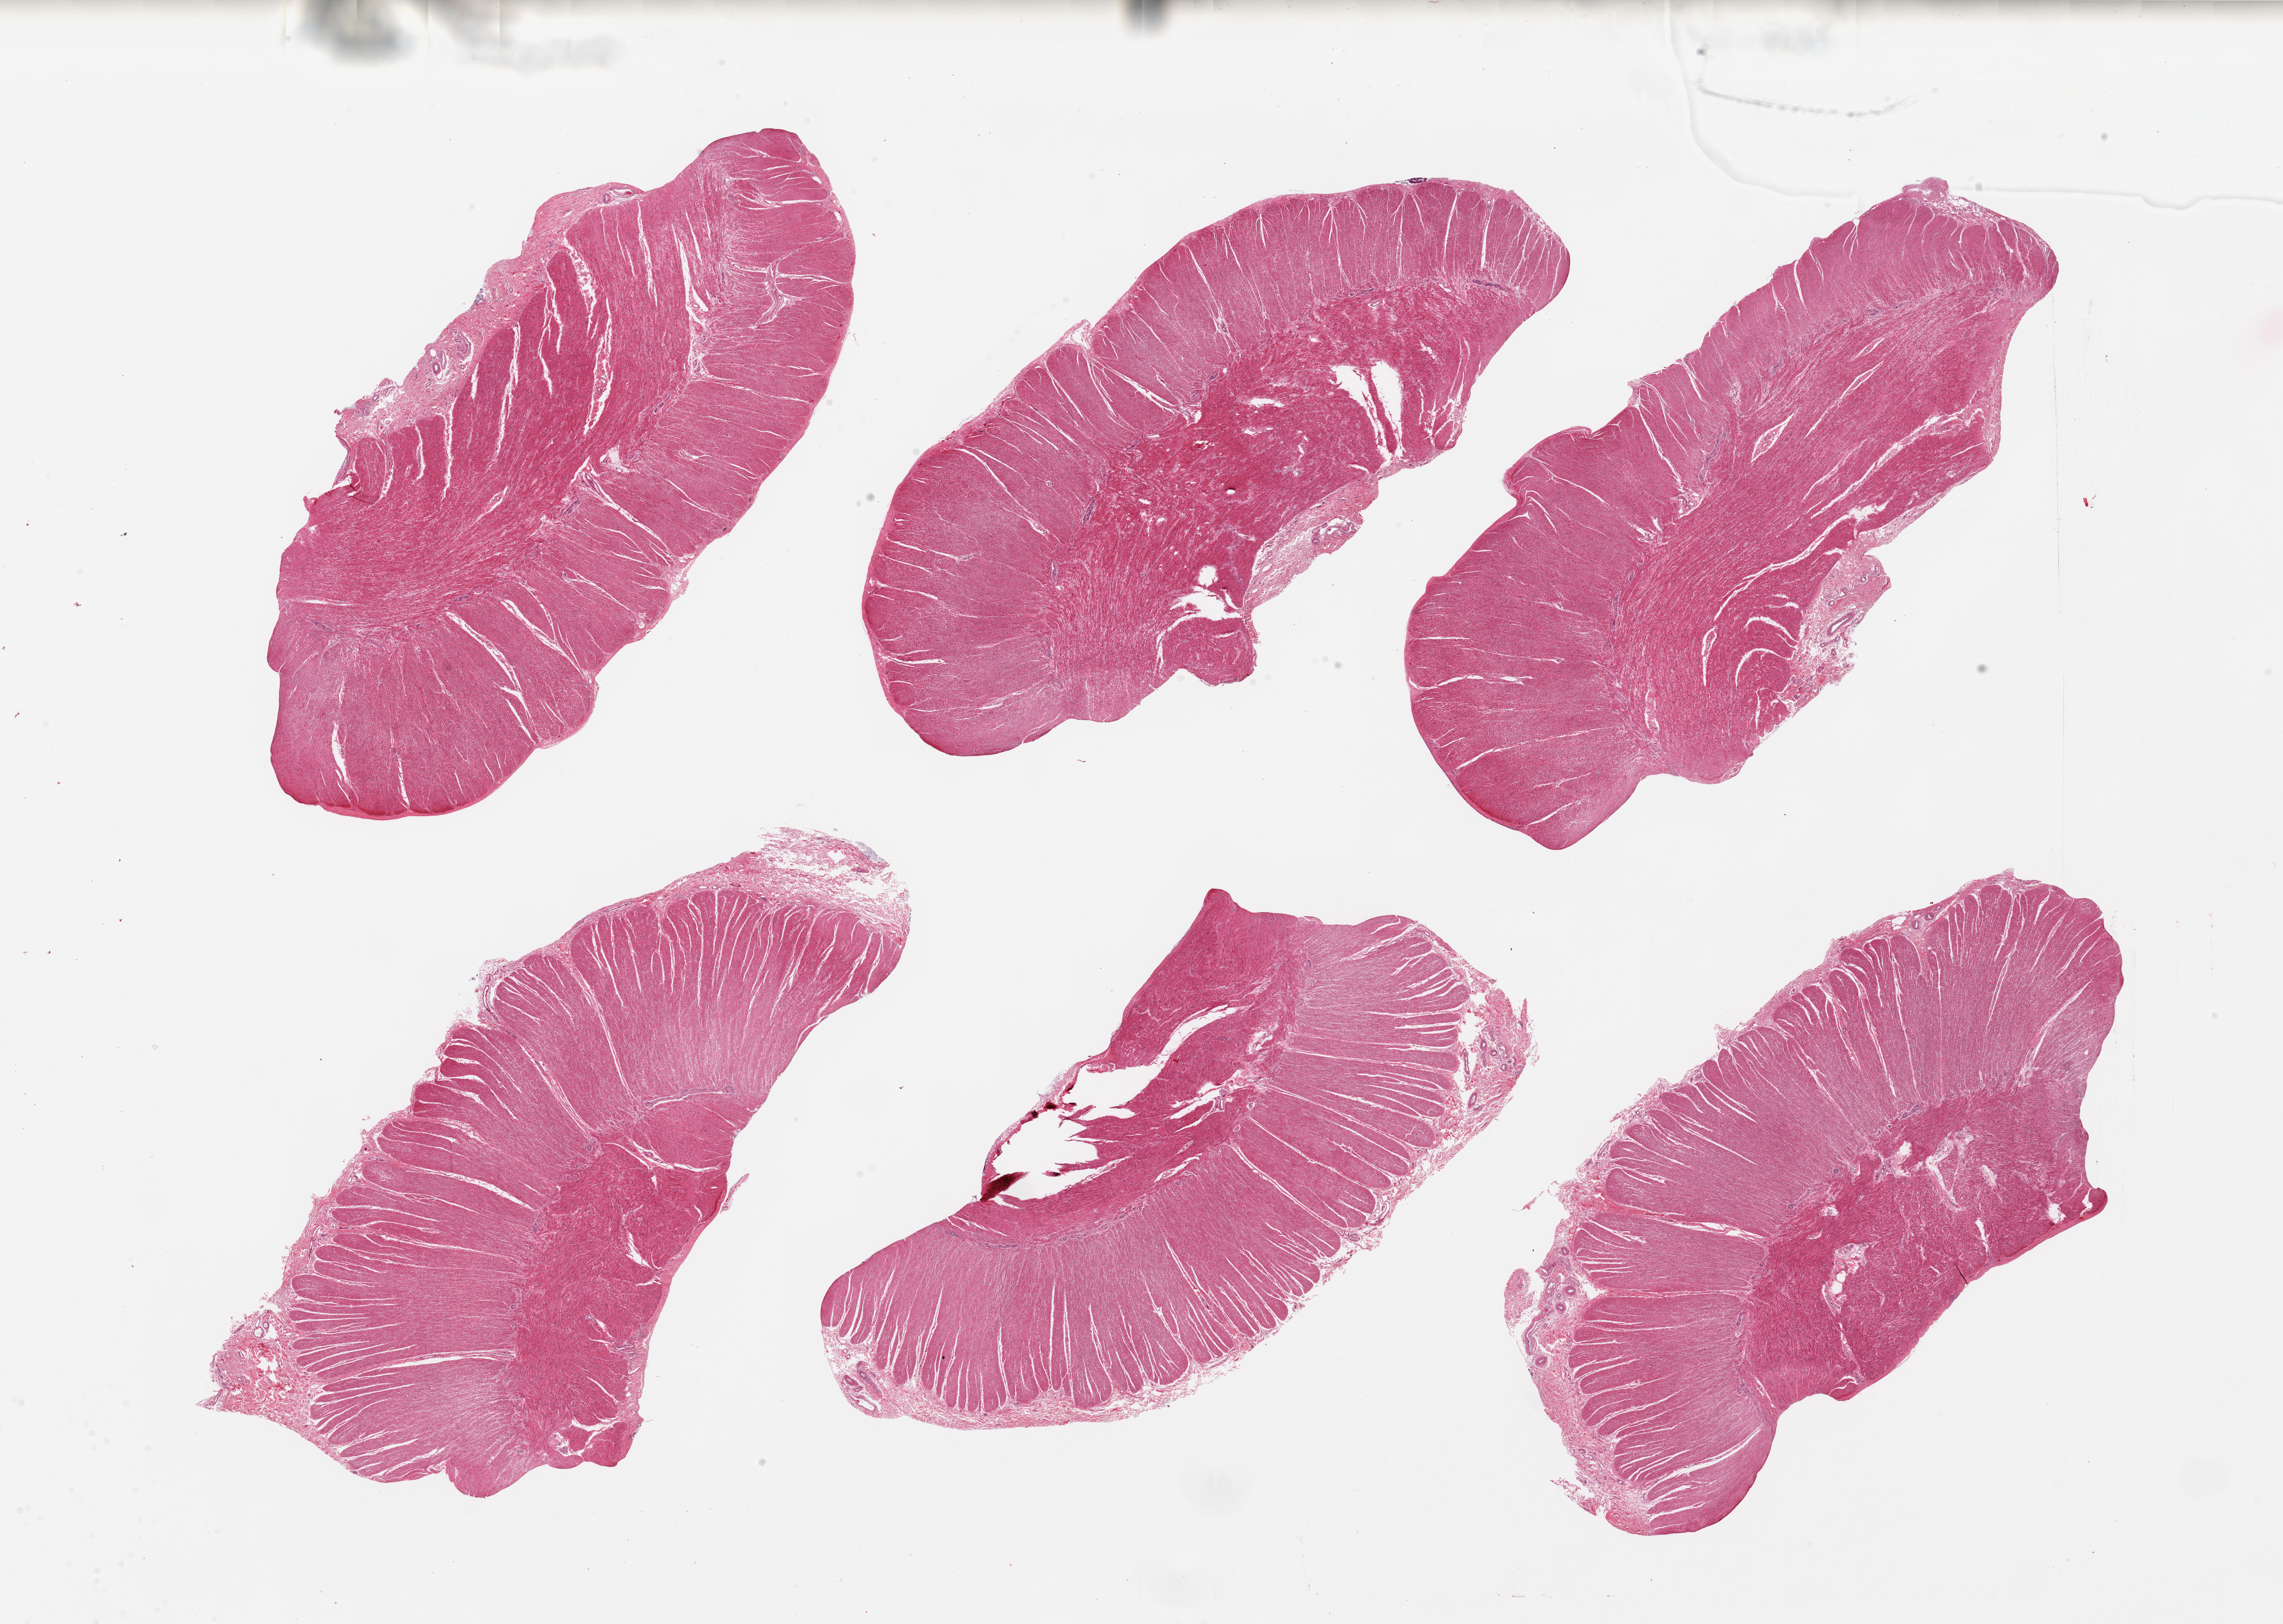
Digitized hematoxylin and eosin (H&E)-stained section, shown as a low-resolution overview of the whole scanned area (about 31.5 x 22.4 mm, acquisition: 20x scan). PAXgene-fixed, paraffin-embedded tissue. Sampled site (target tissue): sigmoid colon. Donor tissue sample. Donor sex: male.
Reviewer comment on this tissue sample: 6 pieces; well trimmed.